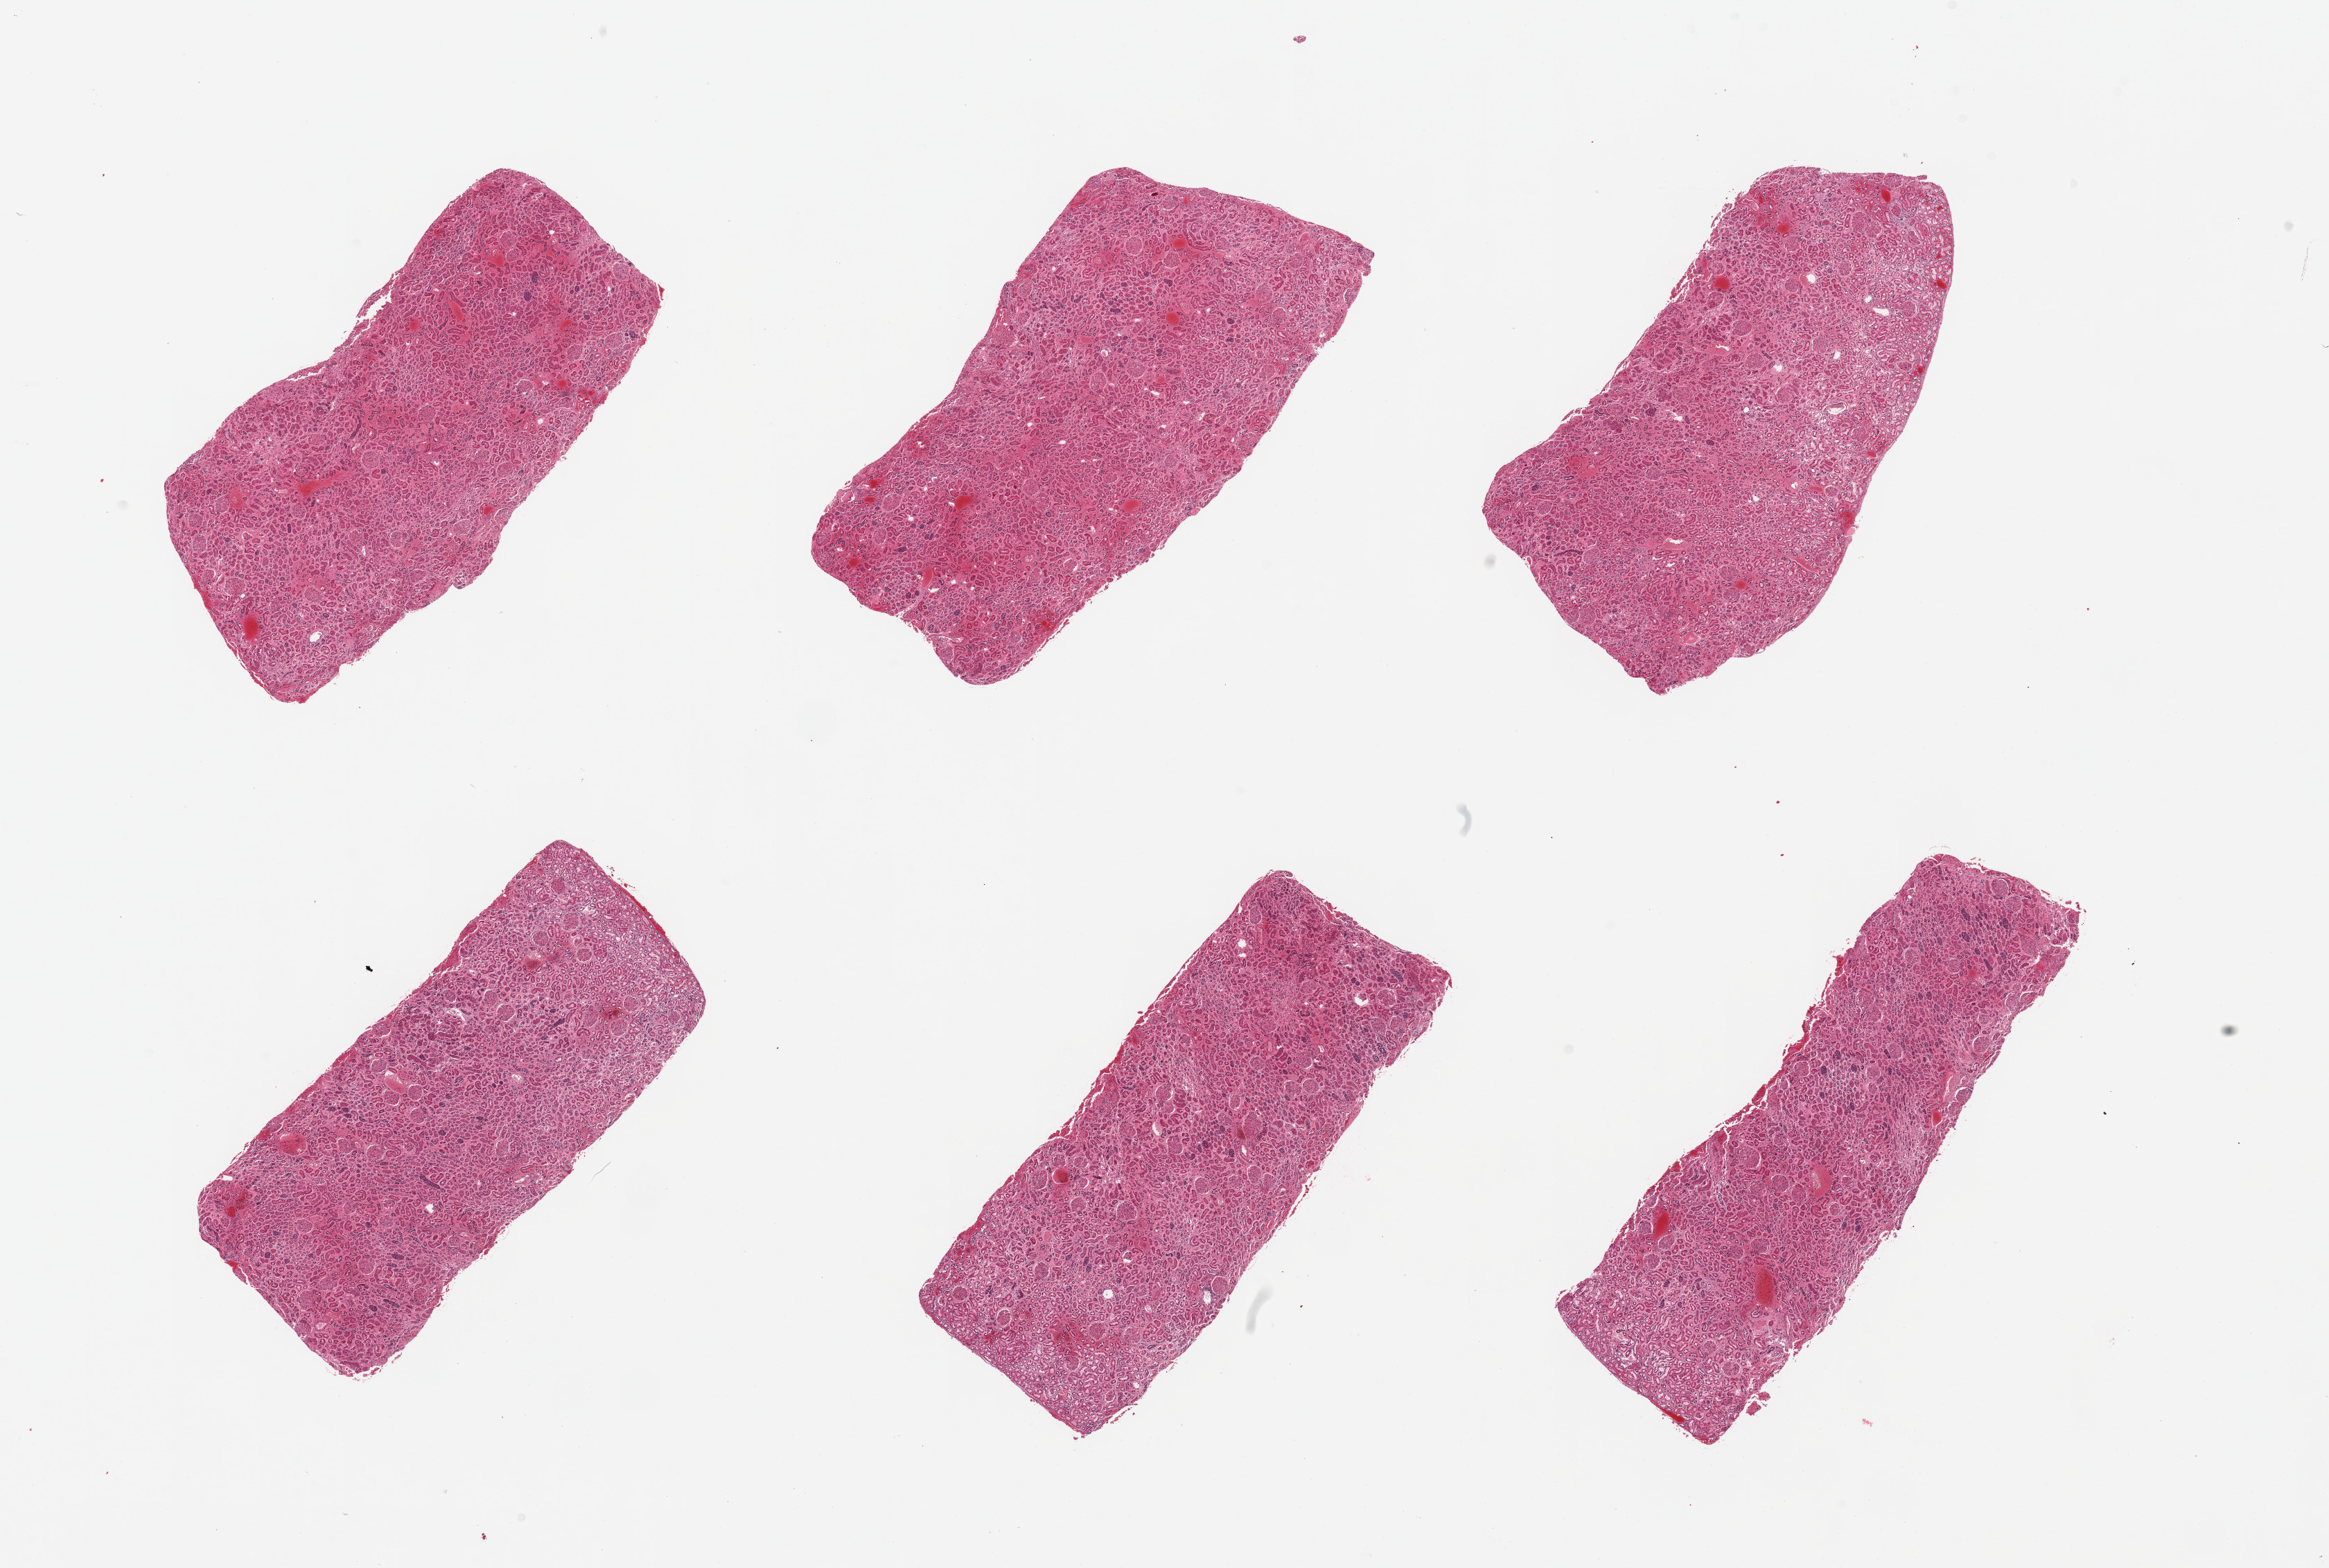
Whole-slide image, haematoxylin and eosin stain, a low-resolution overview of the entire scanned area, about 26.6 x 17.9 mm (from a 20x scan), PAXgene-fixed, paraffin-embedded tissue, section of renal cortex (target tissue), donor tissue sample. Donor: female.
• review note (as recorded): 6 pieces; no sign of chronic disease